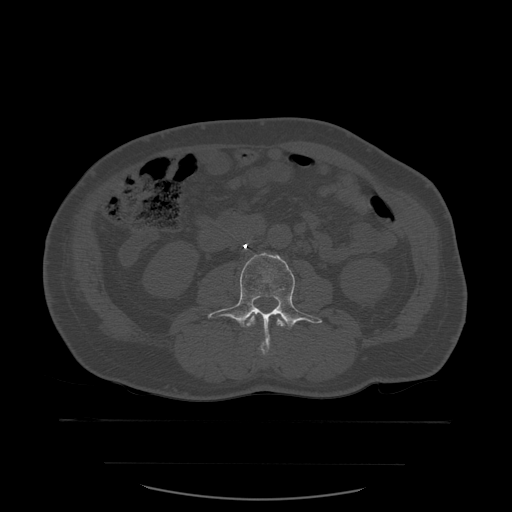
CT including the spine, one axial slice; position 197 of 590 along the scan axis; bone window (W 1800 / L 400 HU); 1.25 mm slice thickness; 512 × 512 image matrix. Patient age 71 years. Case-level facts recorded for this patient, not image findings: primary cancer: lung; vertebrae with lytic lesions (as recorded): T1, T2, L5, S1.
Annotated regions visible in this slice (semi-automatically segmented with operator editing):
- L2 vertebra: bounding box (x1, y1, x2, y2) in pixels: (246, 311, 291, 358)
- L3 vertebra: (208, 253, 323, 348)